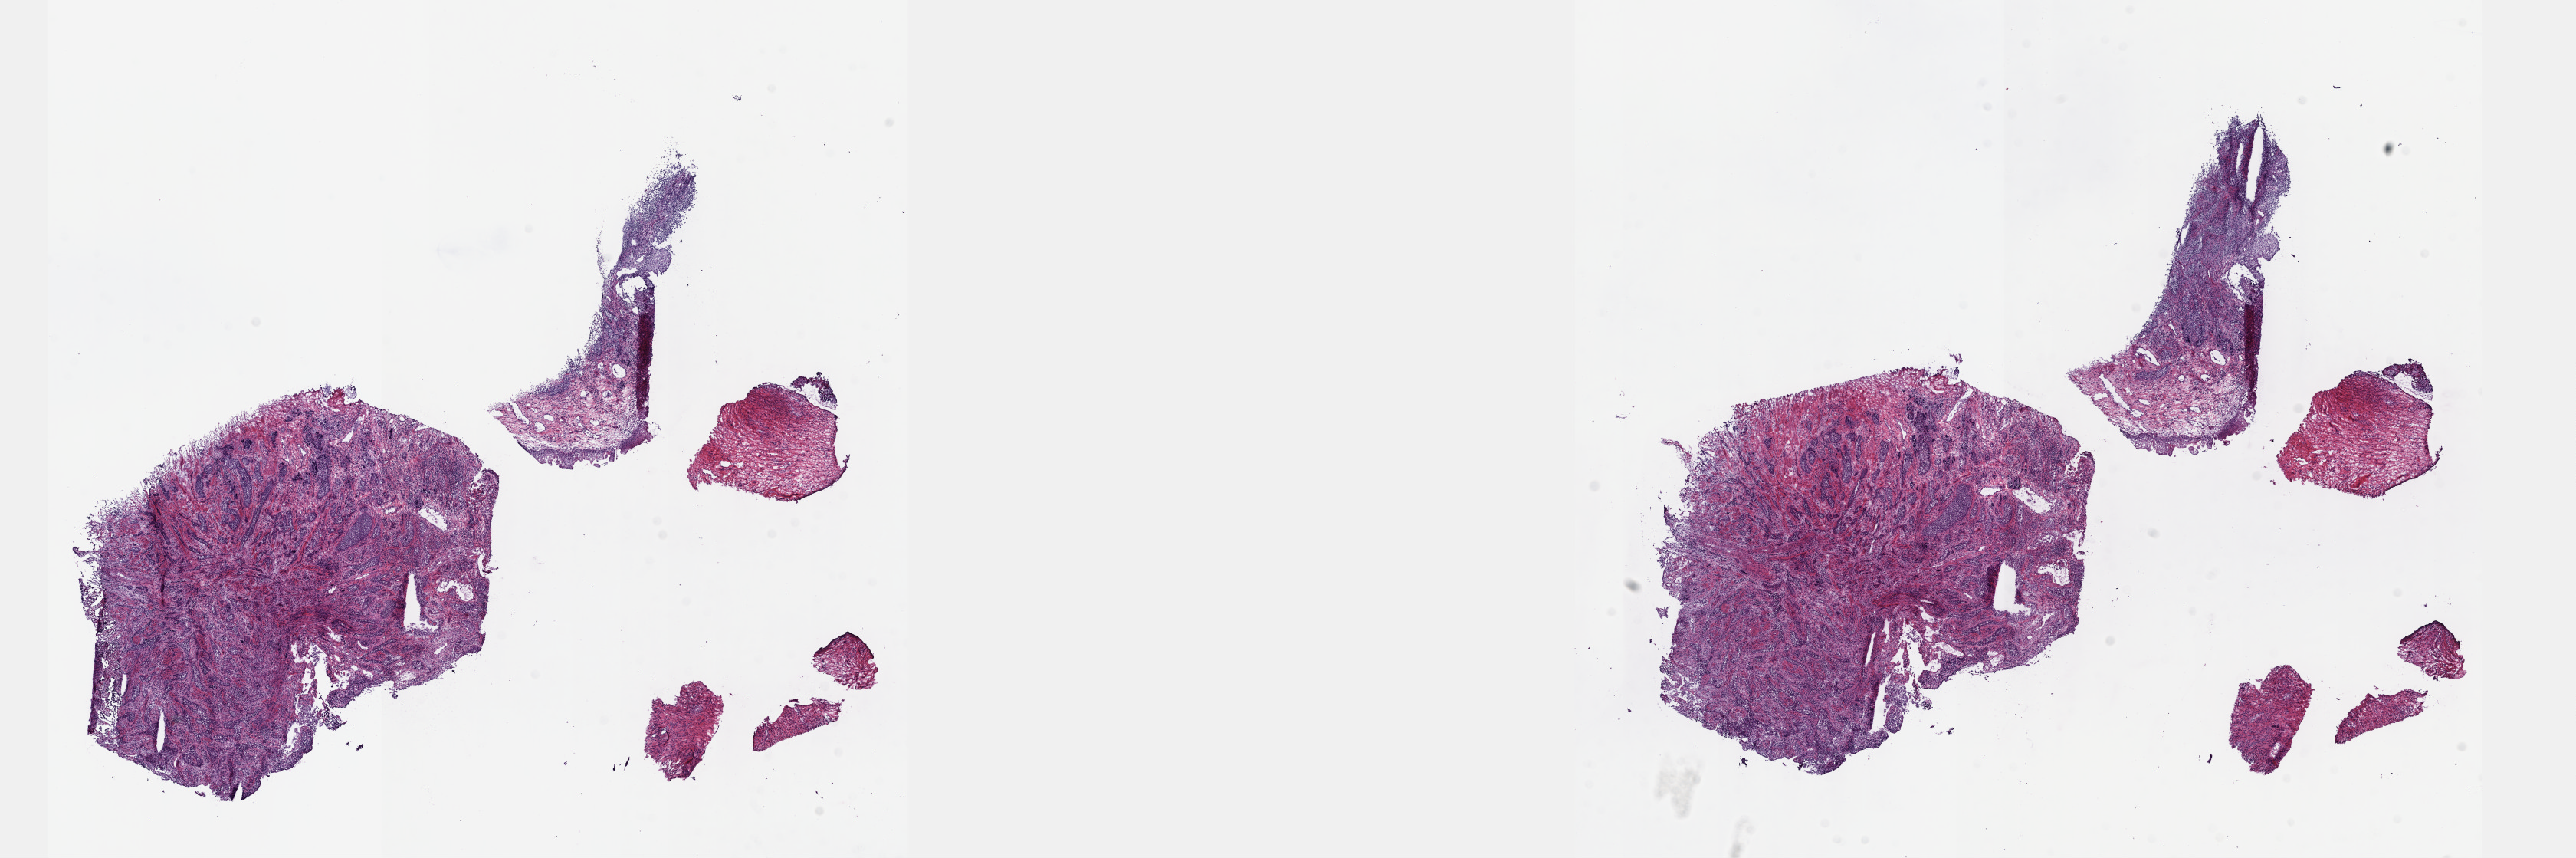
Whole-slide histology image, H&E — a low-resolution overview of the entire scanned area, about 27.2 x 9.0 mm, frozen section from the top of the tissue portion, cervix, primary tumour sample. Female, age 64 years at initial diagnosis. Slide review estimates, as recorded: tumour cells 60%, tumour nuclei 60%.
Pathologic diagnosis: Squamous cell carcinoma, NOS (cervix uteri).